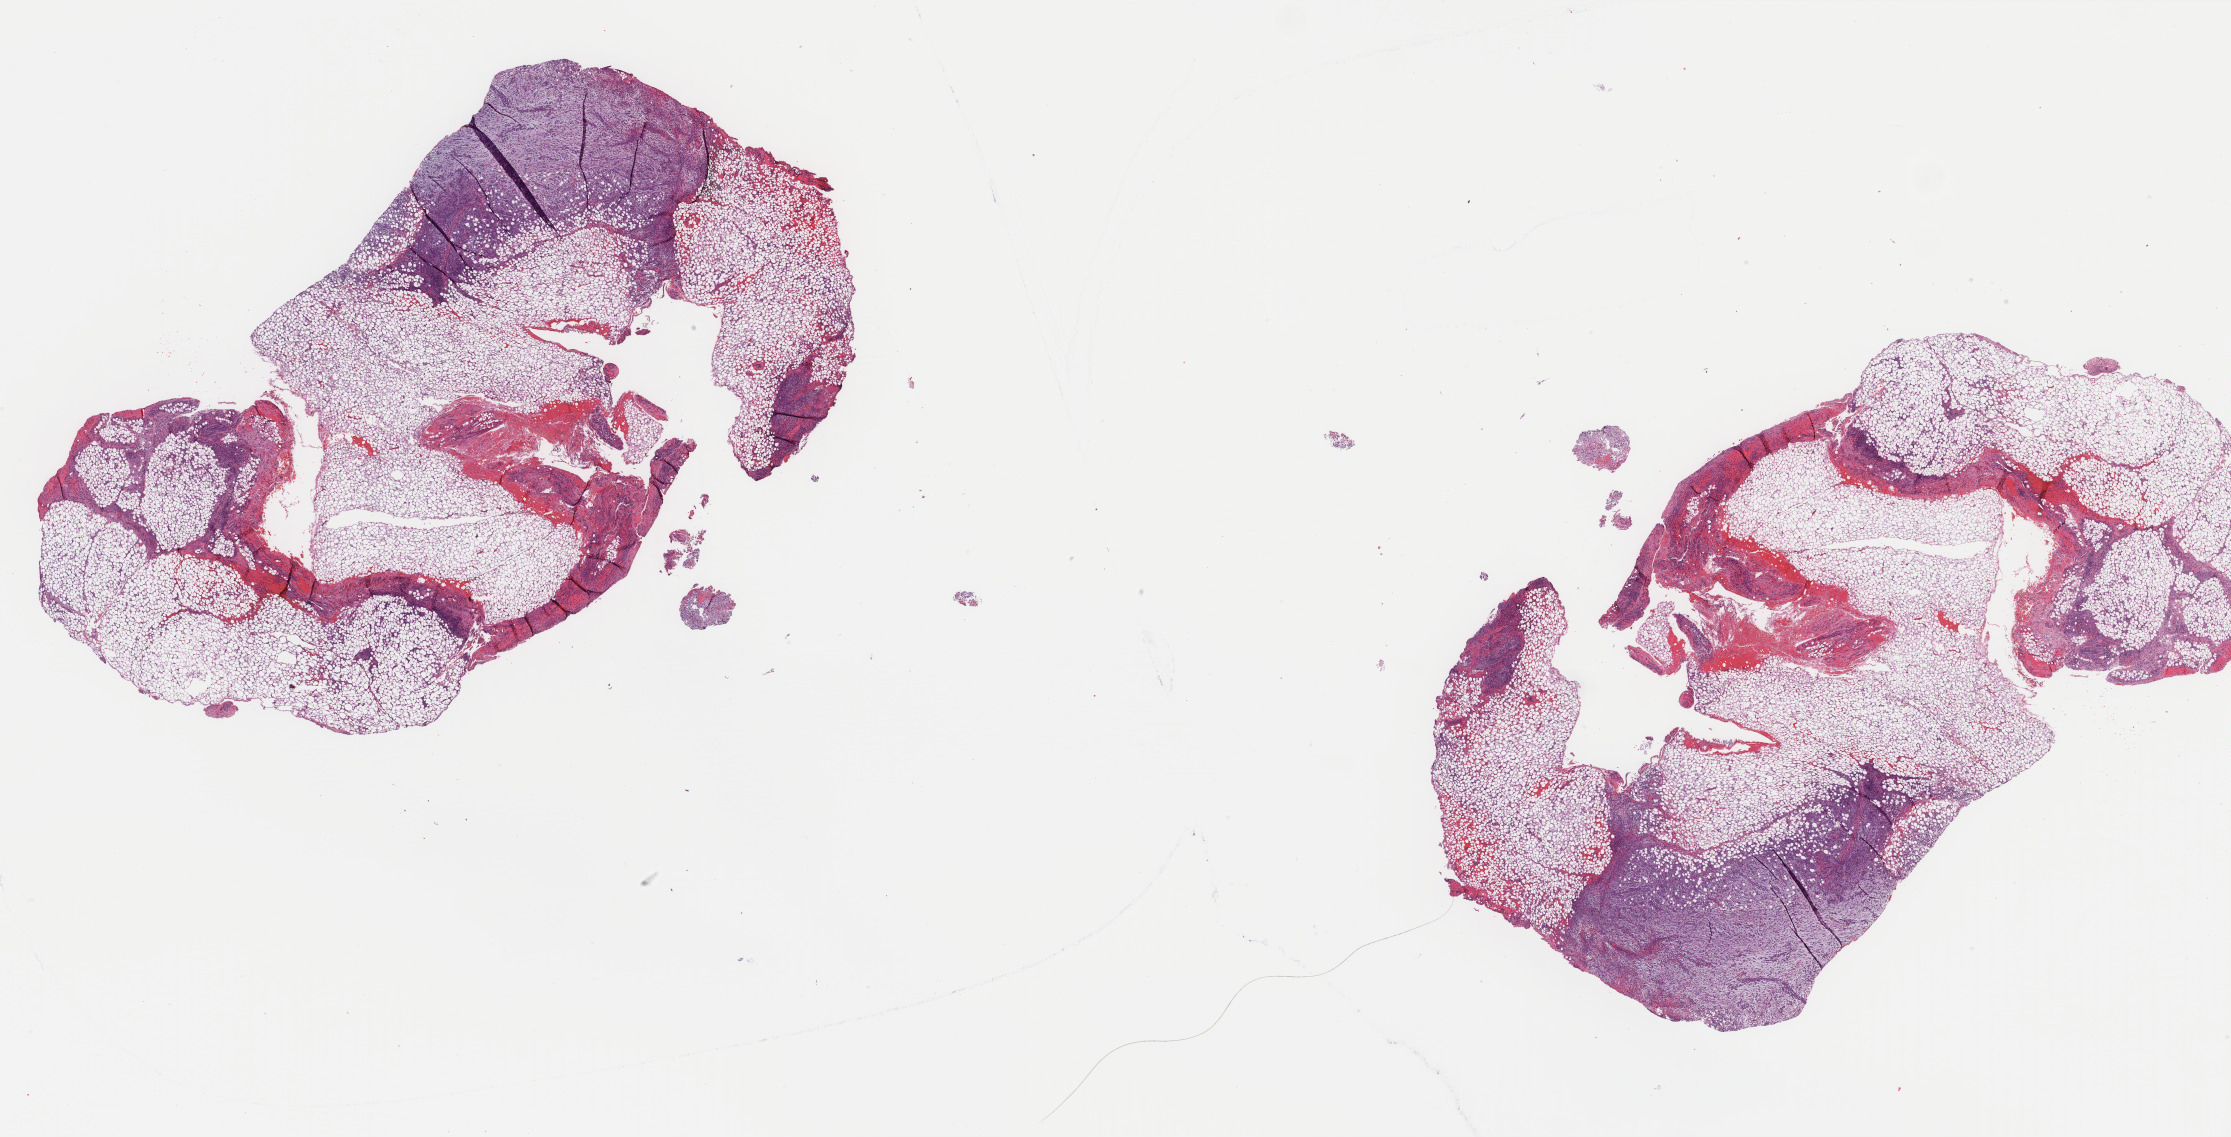
Whole-slide histology image, H&E-stained, a low-resolution overview of the entire scanned area, about 35.4 x 18.0 mm (acquisition: 40x scan); formalin-fixed paraffin-embedded (FFPE) diagnostic section; skin, primary tumour sample. Female patient; age at initial diagnosis 58 years.
AJCC pathologic stage: IIIC. TNM: T3 N3 M0. Pathologic diagnosis: Malignant melanoma, NOS.